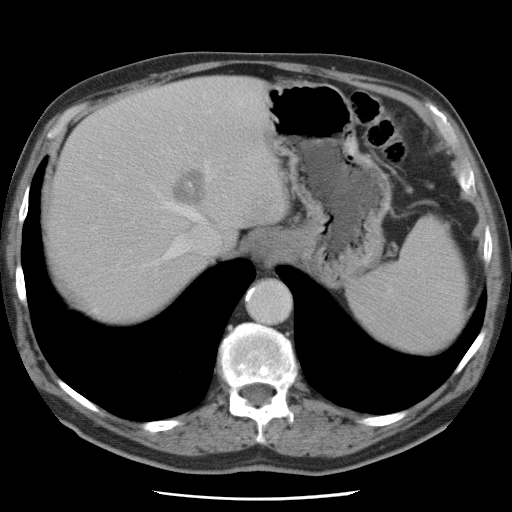
Contrast-enhanced abdominal CT, one axial slice. Position 62 of 78 along the scan axis. Intravenous contrast given. Soft-tissue window (W 400 / L 40 HU). 512 × 512 image matrix. Male patient, age 75 years. From the clinical record (not read from this slice): diagnosis: colorectal cancer liver metastases, imaged before liver resection; multiple liver metastases: yes; largest metastasis: 2.4 cm; disease in both lobes: yes.
Structures marked on this image (manually delineated by an expert):
- hepatic veins: box from (x=115, y=99) to (x=261, y=260) px
- liver: (x=48, y=79)–(x=282, y=317)
- planned liver remnant (the part of the liver to remain after resection): (x=49, y=135)–(x=201, y=319)
- liver metastasis: (x=172, y=169)–(x=206, y=206)